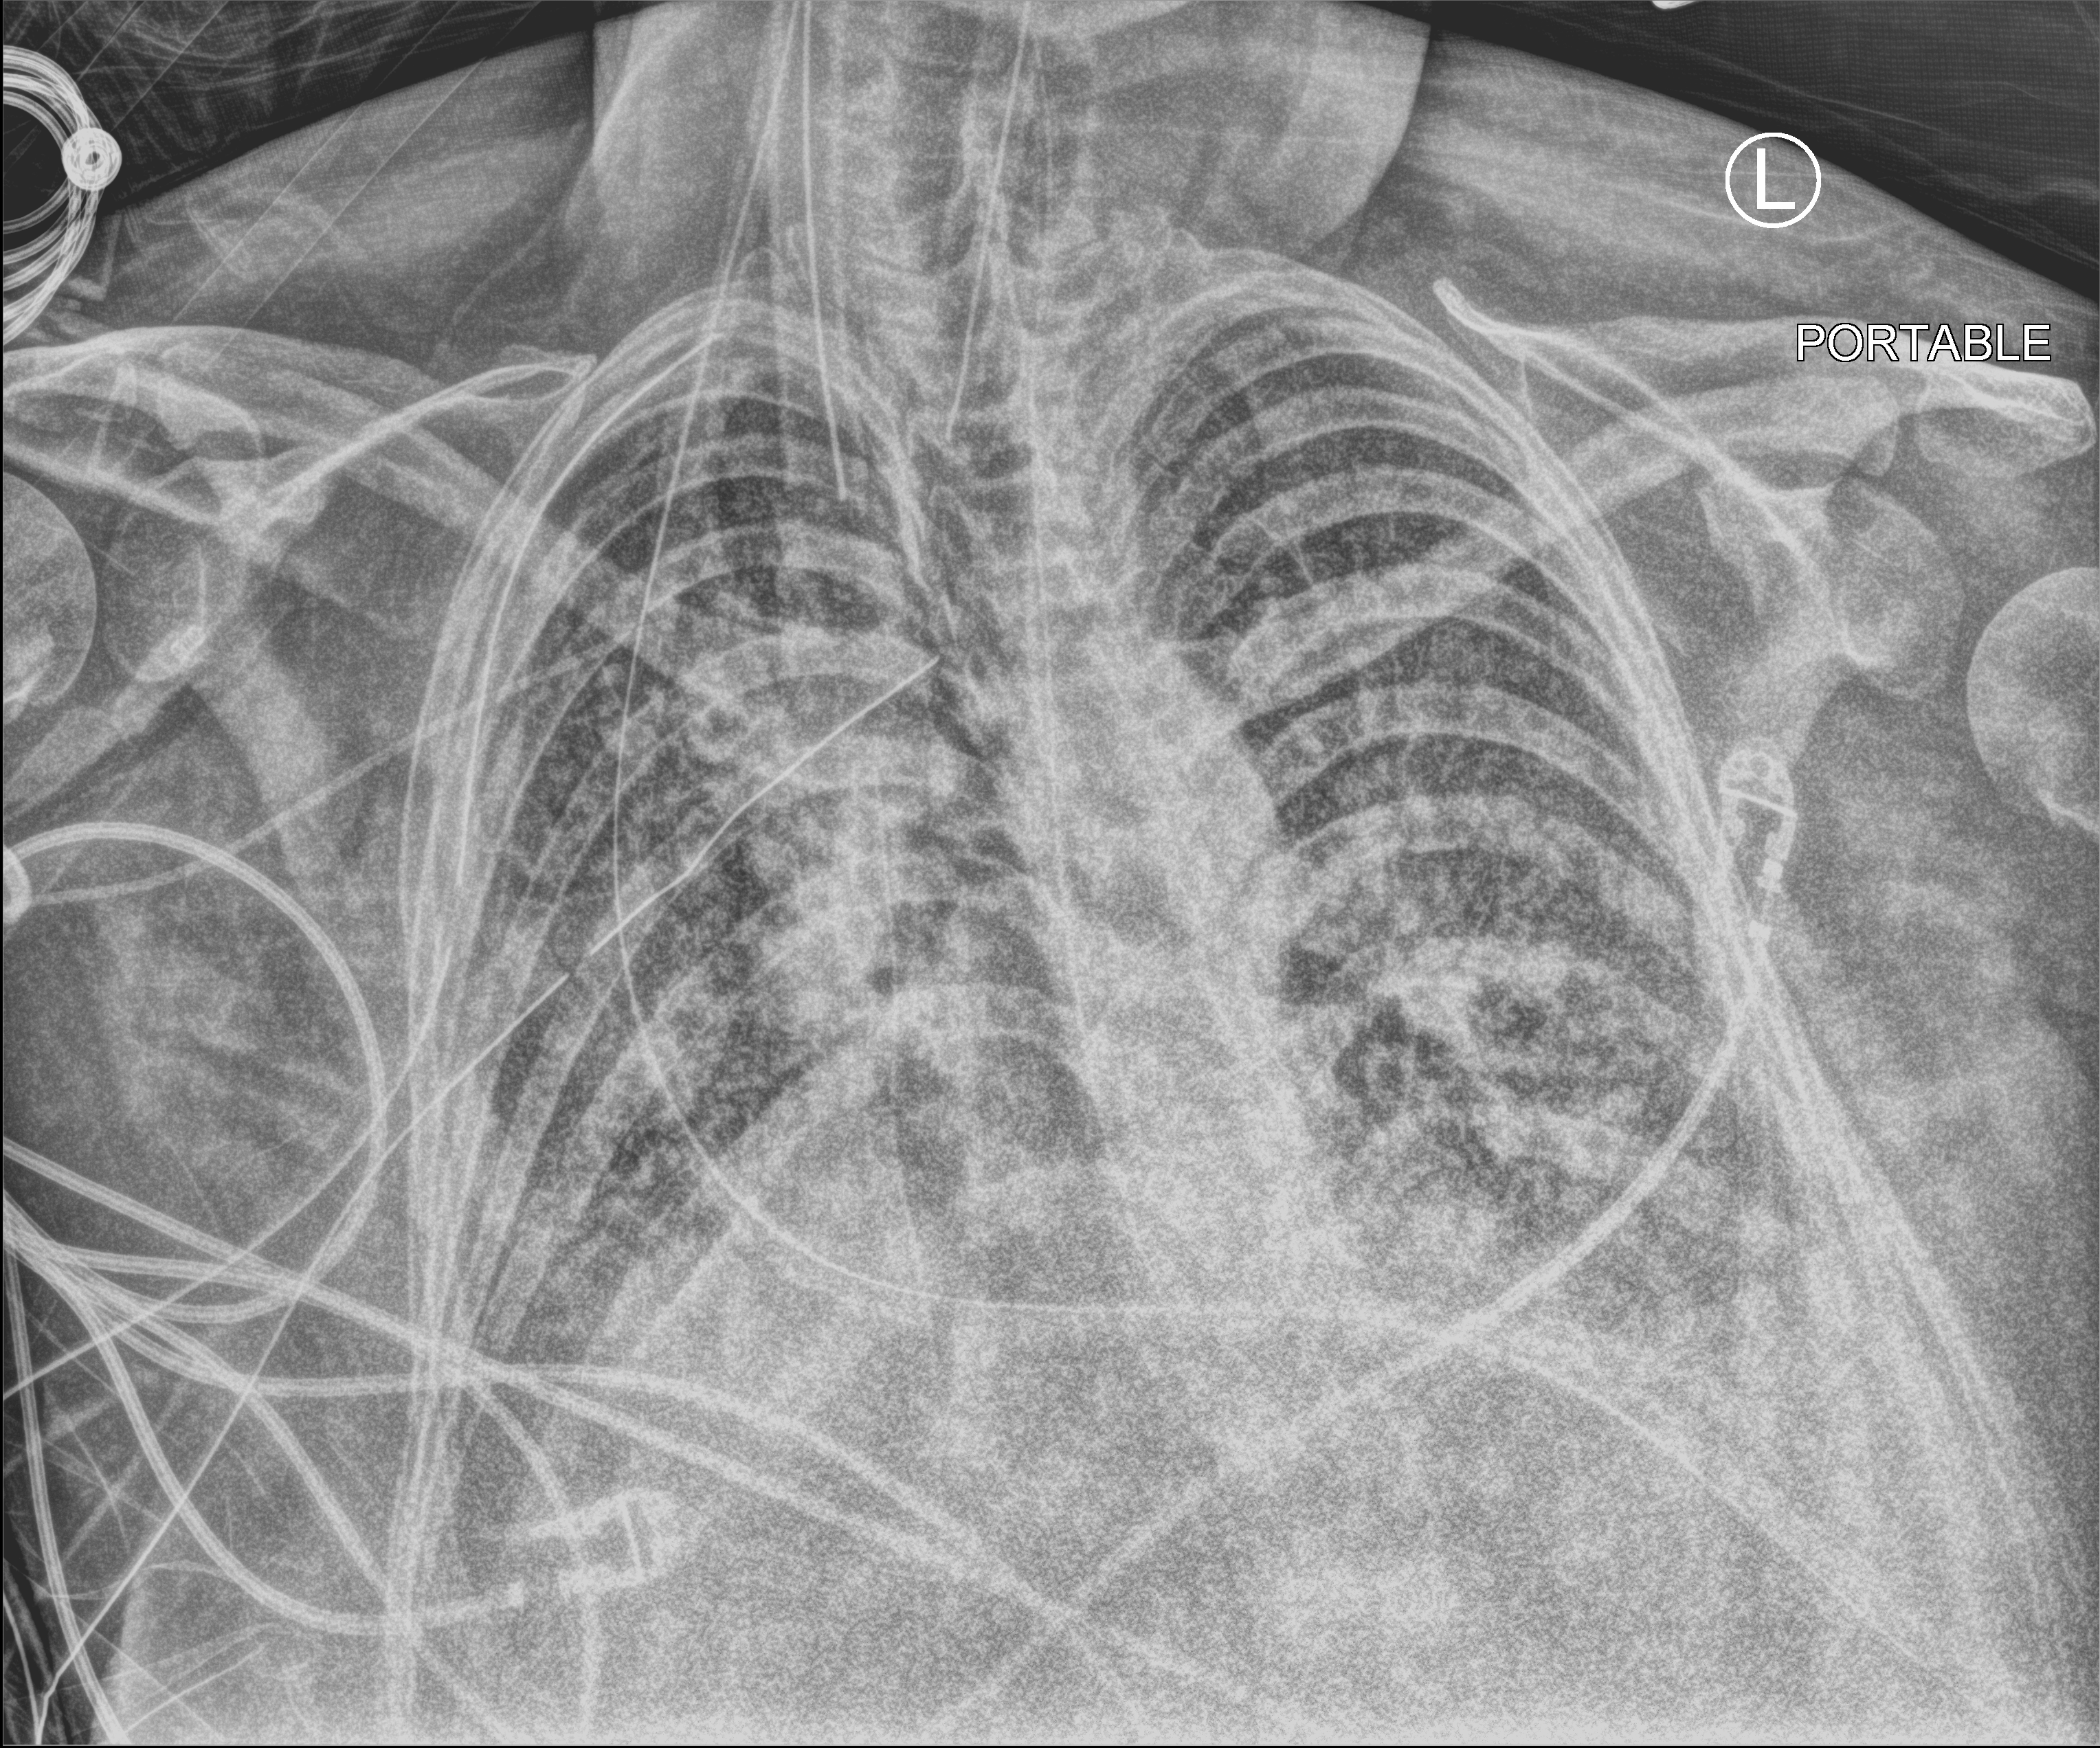
Portable chest radiograph; anteroposterior (AP) projection. Adult patient hospitalised with COVID-19, age 18–59 years.
Admission-level facts for this patient (not findings on this image; timing relative to this image not recorded): admitted to intensive care during this hospital stay: yes; mechanically ventilated during this hospital stay: yes; length of hospital stay: 48 days.